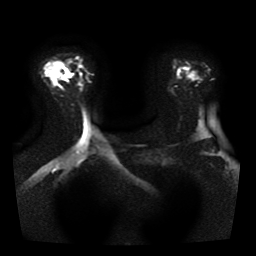
Breast MRI, one axial slice; slice 28 of 41 in the series (ordered by position); diffusion-weighted series; image 2 of 4 stored at this slice position (different b-values; order by instance number); 1.5 T; 256 × 256 image matrix, field of view 330 × 330 mm. Female patient.
Structures marked on this image (manually delineated by an expert):
- tumour on diffusion-weighted imaging: bounding box <62,69,69,81> (left, top, right, bottom; pixels)